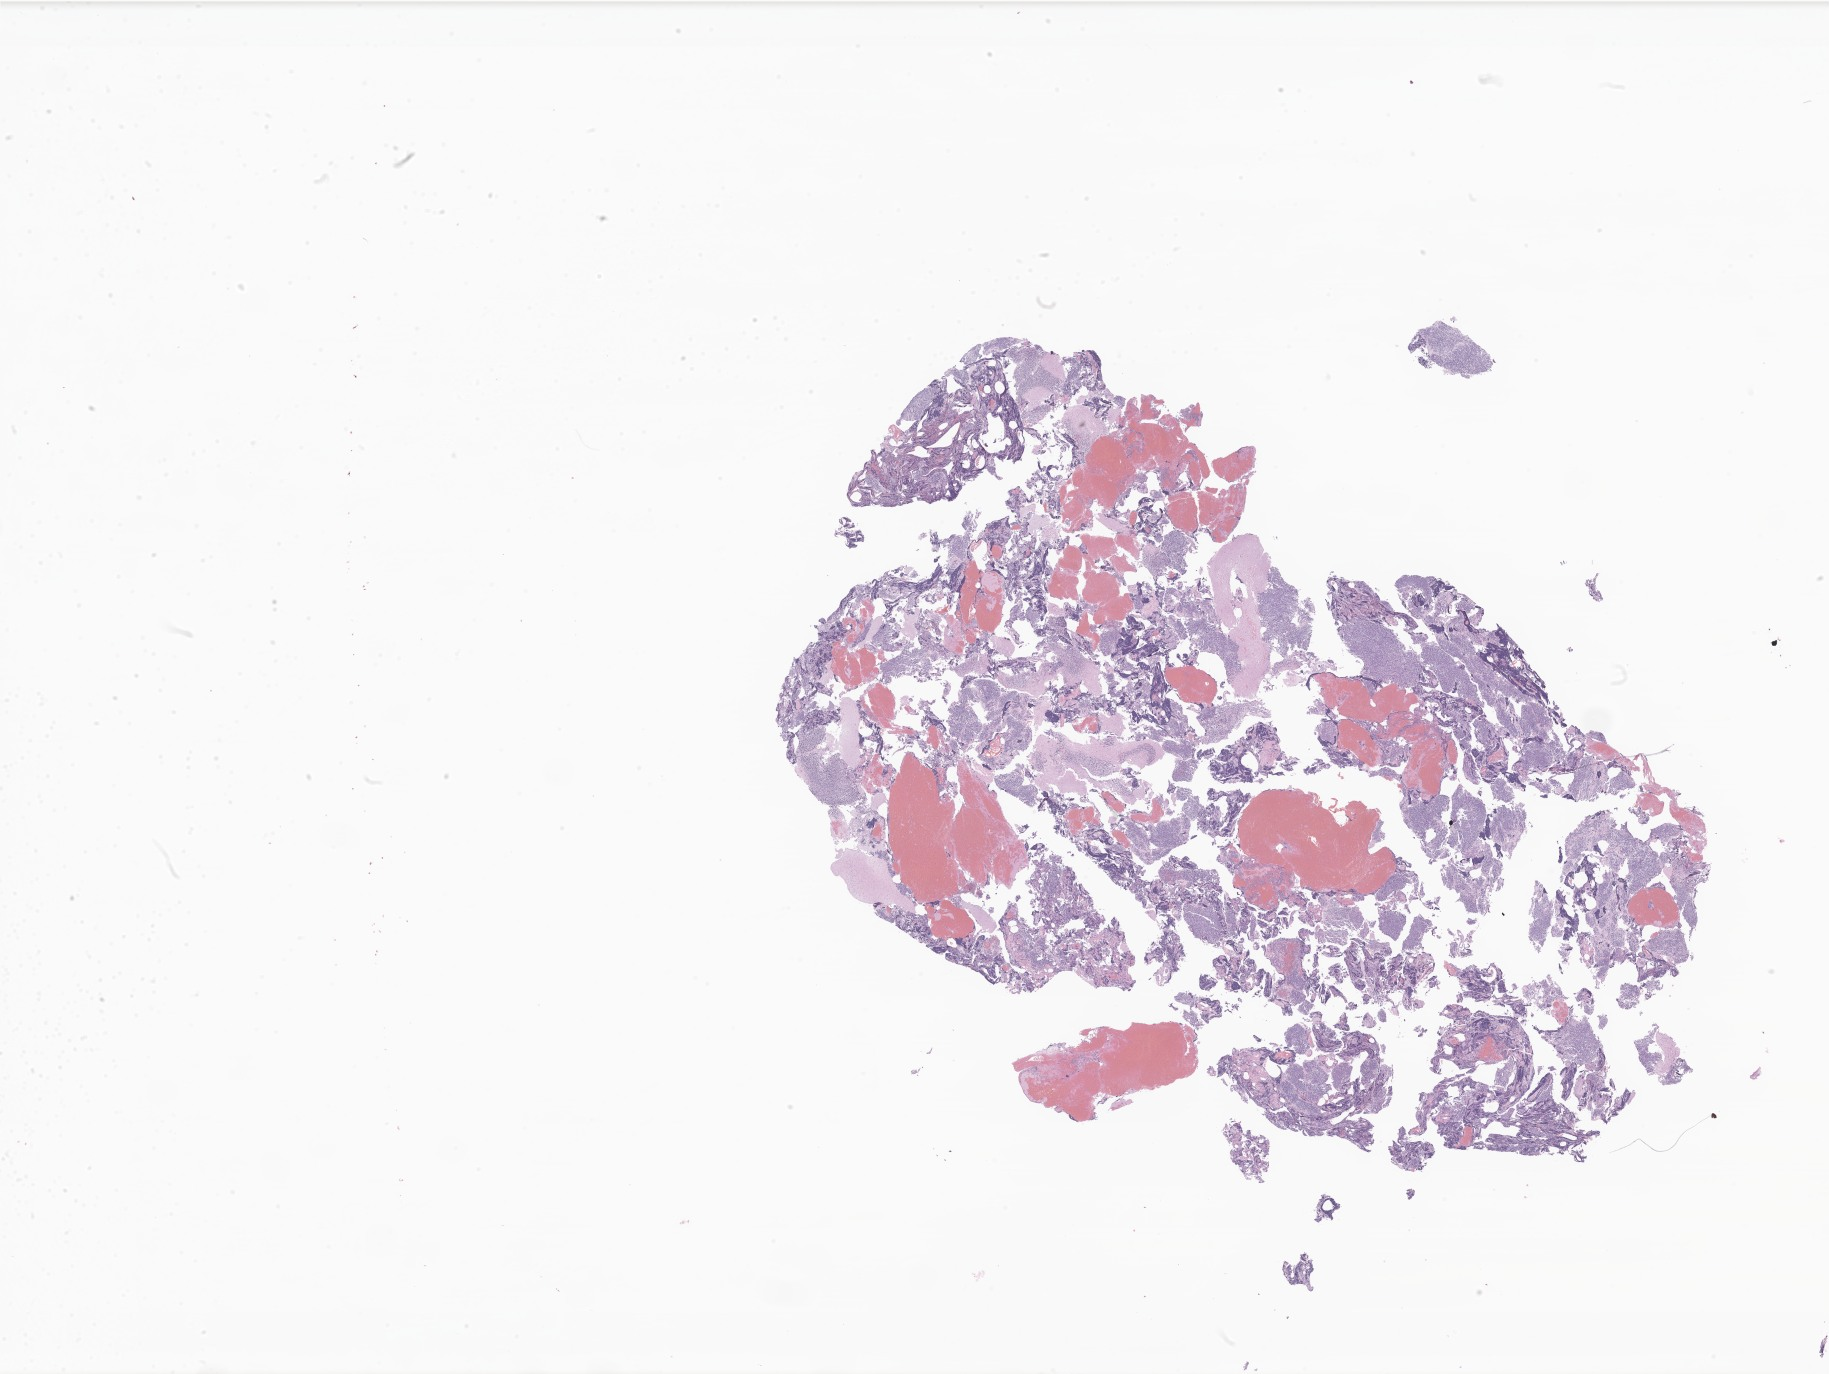
Digitized H&E-stained section of tumor tissue from the brain — low-resolution overview of the scanned area, about 30.8 x 23.2 mm. FFPE section. Female patient, age 97 months (8 years 1 month).
Diagnosis (ICD-O-3 morphology term): Medulloblastoma, NOS.